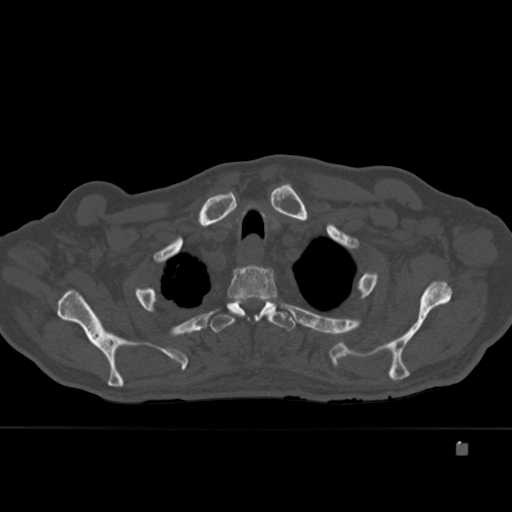
CT including the spine, one axial slice. Slice 341 of 451 in the series (ordered by position). Bone window (W 1800 / L 400 HU). 512 × 512 image matrix. Patient: male, 75 years. From the clinical record (not read from this slice): primary cancer: prostate.
Outlined on this slice (semi-automatic segmentation, software-assisted and operator-edited):
- T2 vertebra: box from (x=227, y=265) to (x=277, y=321) px
- T3 vertebra: (x=210, y=298)–(x=296, y=333)